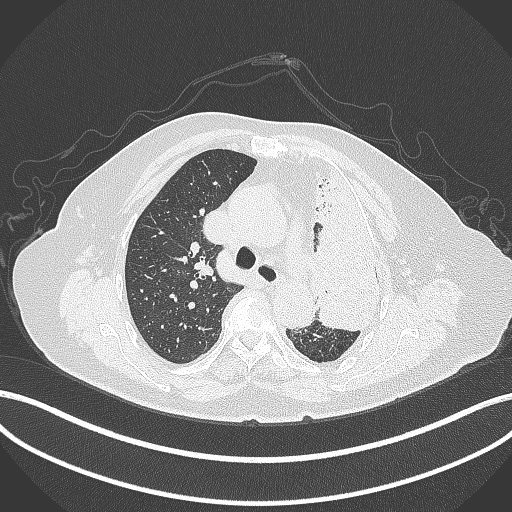
Chest CT, one axial slice; position 276 of 399 along the scan axis; reconstruction kernel B70f; lung window (W 1500 / L -600 HU); 1 mm slice thickness; 512 × 512 image matrix, field of view 400 × 400 mm. Female patient, age 75 years. From the clinical record (not read from this slice): clinical TNM (as recorded): T3 N3 M1.
Annotated regions visible in this slice (bounding box drawn by a radiologist):
- lung tumour (recorded histology: adenocarcinoma): box from (x=306, y=160) to (x=383, y=330) px